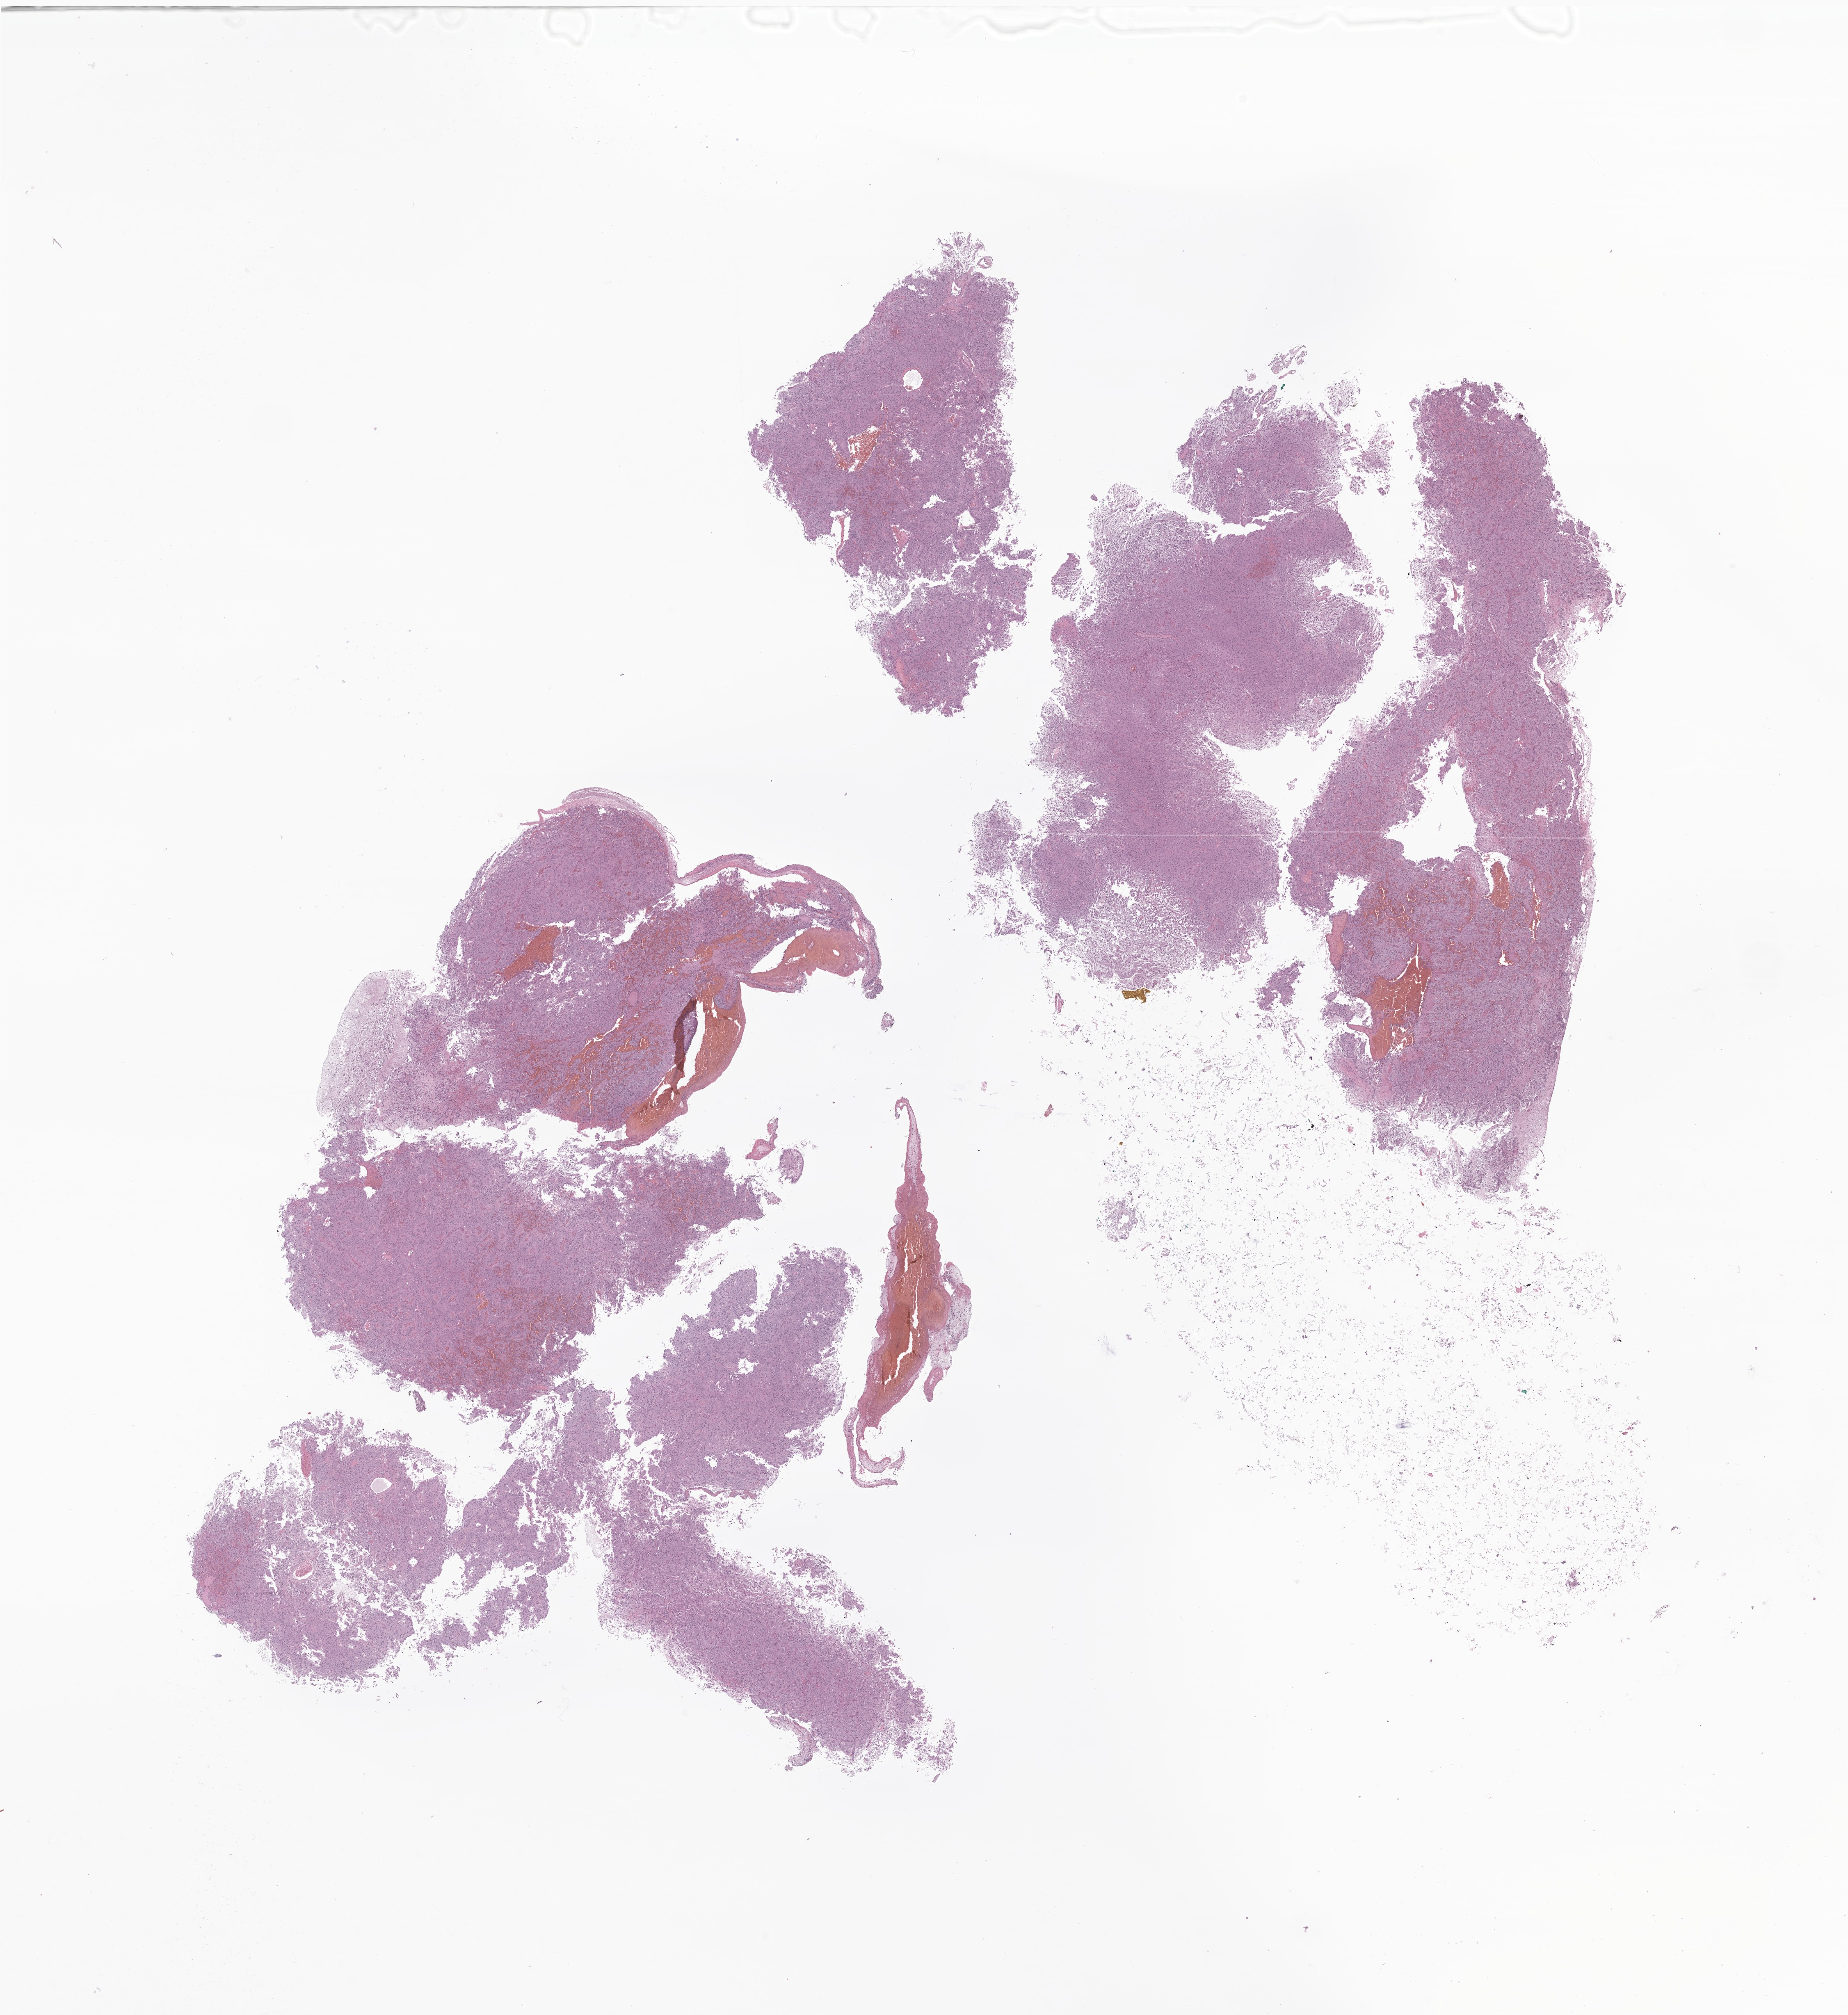
Whole-slide image, H&E stain of tumor tissue from the cerebral ventricle, low-resolution overview of the scanned area, about 19.0 x 20.7 mm; formalin-fixed paraffin-embedded section. Patient male; age 111 months (9 years 3 months).
Diagnosis (ICD-O-3 morphology term): Subependymal giant cell astrocytoma.